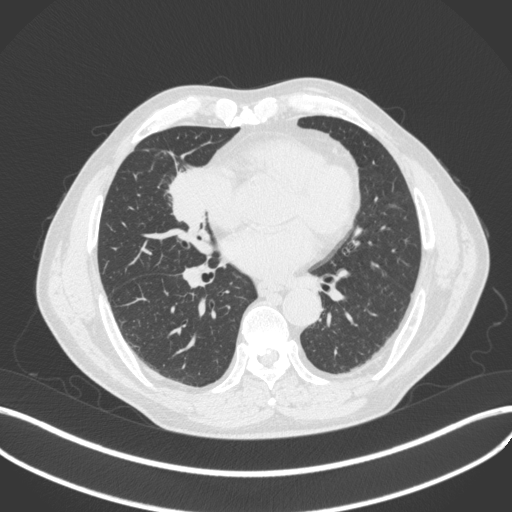
Chest CT, one axial slice; slice 182 of 429 in the series (ordered by position); 120 kVp; lung window (W 1500 / L -600 HU); 1 mm slice thickness; 512 × 512 image matrix. Male patient, age 61 years. Case-level facts recorded for this patient, not image findings: clinical TNM (as recorded): T2b N1 M0.
Outlined on this slice (bounding box drawn by a radiologist):
- lung tumour (recorded histology: squamous cell carcinoma): bounding box (x1, y1, x2, y2) in pixels: (159, 153, 214, 229)